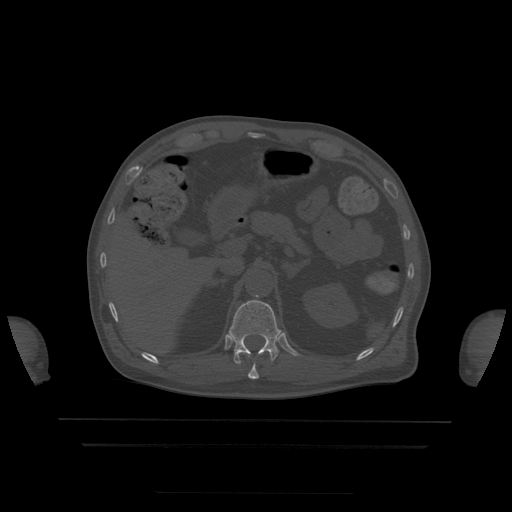
CT including the spine, one axial slice. Slice 202 of 522 in the series (ordered by position). Bone window (W 1800 / L 400 HU). 1.25 mm slice thickness. 512 × 512 image matrix, field of view 436 × 436 mm. Patient age 68 years. Case-level facts recorded for this patient, not image findings: primary cancer: urothelial.
Structures marked on this image (semi-automatic segmentation, software-assisted and operator-edited):
- T11 vertebra: bounding box [x1, y1, x2, y2] px = [248, 364, 259, 379]
- T12 vertebra: [229, 296, 281, 364]